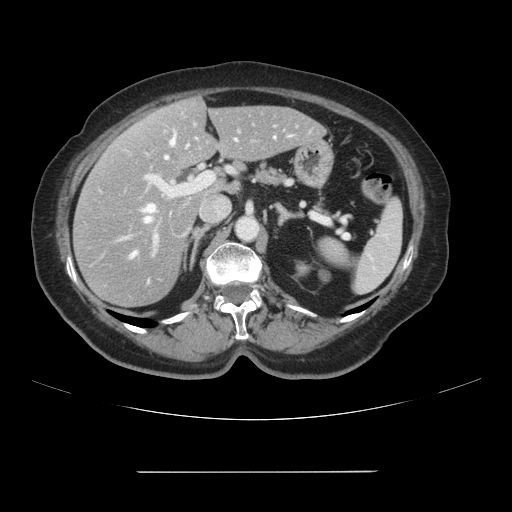
Contrast-enhanced abdominal CT, one axial slice. 120 kVp. Soft-tissue window (W 400 / L 40 HU). 2.5 mm slice thickness. 512 × 512 image matrix, field of view 400 × 400 mm. Female patient, age 74 years. Case-level facts recorded for this patient, not image findings: diagnosis: colorectal cancer liver metastases, imaged before liver resection; multiple liver metastases: yes; largest metastasis: 1.1 cm; disease in both lobes: yes.
Annotated regions visible in this slice (outlined manually by an expert reader):
- hepatic veins: box from (x=132, y=137) to (x=275, y=257) px
- liver: (x=74, y=99)–(x=323, y=307)
- planned liver remnant (the part of the liver to remain after resection): (x=146, y=99)–(x=323, y=194)
- portal vein (with intrahepatic branches): (x=122, y=123)–(x=299, y=252)